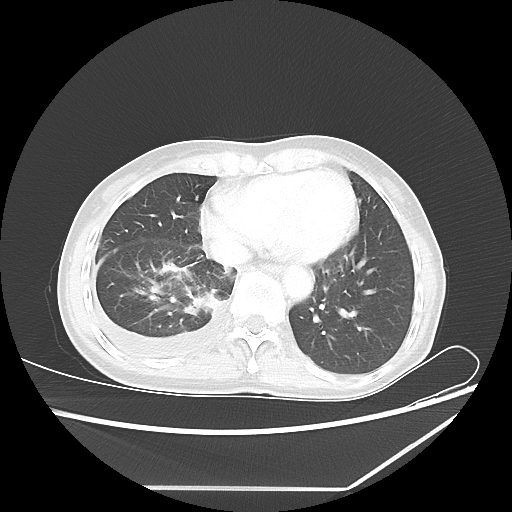
Chest CT, one axial slice; slice 20 of 60 in the series (ordered by position); reconstruction kernel LUNG; lung window (W 1500 / L -600 HU); 5 mm slice thickness; 512 × 512 image matrix, field of view 364 × 364 mm. Patient: female, 59 years. From the clinical record (not read from this slice): clinical TNM (as recorded): T1c N1 M1.
Structures marked on this image (bounding box drawn by a radiologist):
- lung tumour (recorded histology: adenocarcinoma): bounding box <190,287,225,318> (left, top, right, bottom; pixels)